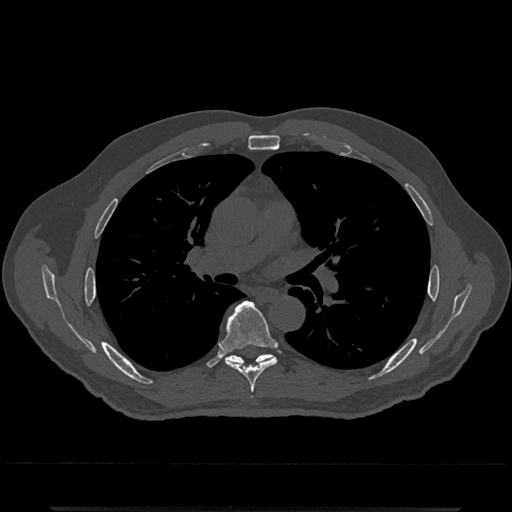
CT including the spine, one axial slice. Position 759 of 797 along the scan axis. 120 kVp. Bone window (W 1800 / L 400 HU). 512 × 512 image matrix, field of view 393 × 393 mm. Patient: male, 67 years. Case-level facts recorded for this patient, not image findings: primary cancer: prostate.
Annotated regions visible in this slice (semi-automatically segmented with operator editing):
- T6 vertebra: box from (x=223, y=301) to (x=277, y=399) px
- T7 vertebra: (x=226, y=354)–(x=272, y=365)